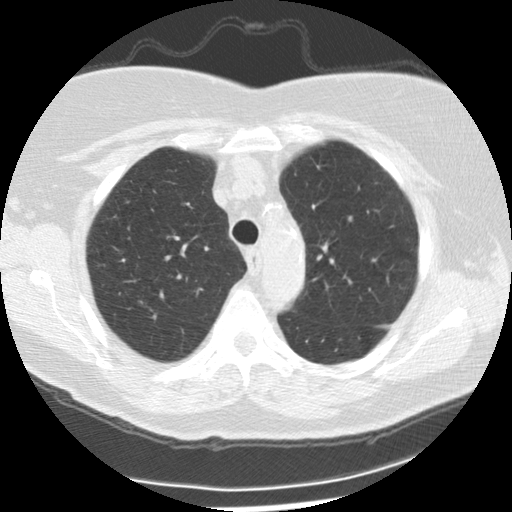
Chest CT (low-dose screening protocol), one axial image; first (baseline) screen; lung window (W 1500 / L -600 HU); 2.5 mm slice thickness; standard (soft-tissue) reconstruction kernel (STANDARD). Female, age 72 years at enrolment.
Lesion marked by an expert reader, bounding box <123,290,155,318> (left, top, right, bottom; pixels). No non-calcified nodule or mass ≥4 mm was recorded by the screening reader at this exam. Official screen result: negative screen, minor abnormalities not suspicious for lung cancer.